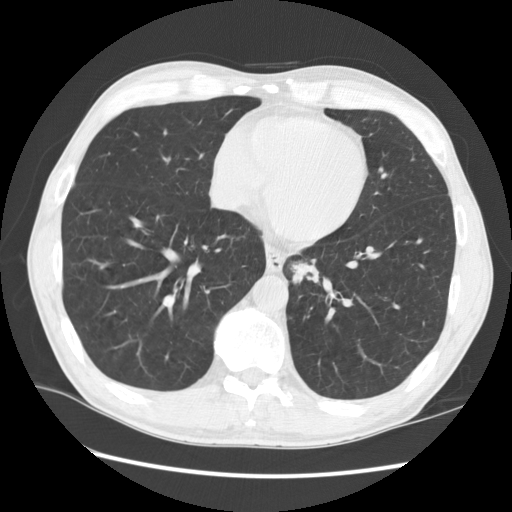
Low-dose screening chest CT, one axial slice. Position 45 of 141 along the scan axis. Lung window (W 1500 / L -600 HU). 2.5 mm slice thickness. 512 × 512 image matrix, field of view 360 × 360 mm.
Annotated regions visible in this slice (expert manual segmentation):
- lesion 2 (nodule, lower lobe of left lung): bounding box (x1, y1, x2, y2) in pixels: (289, 261, 317, 283)